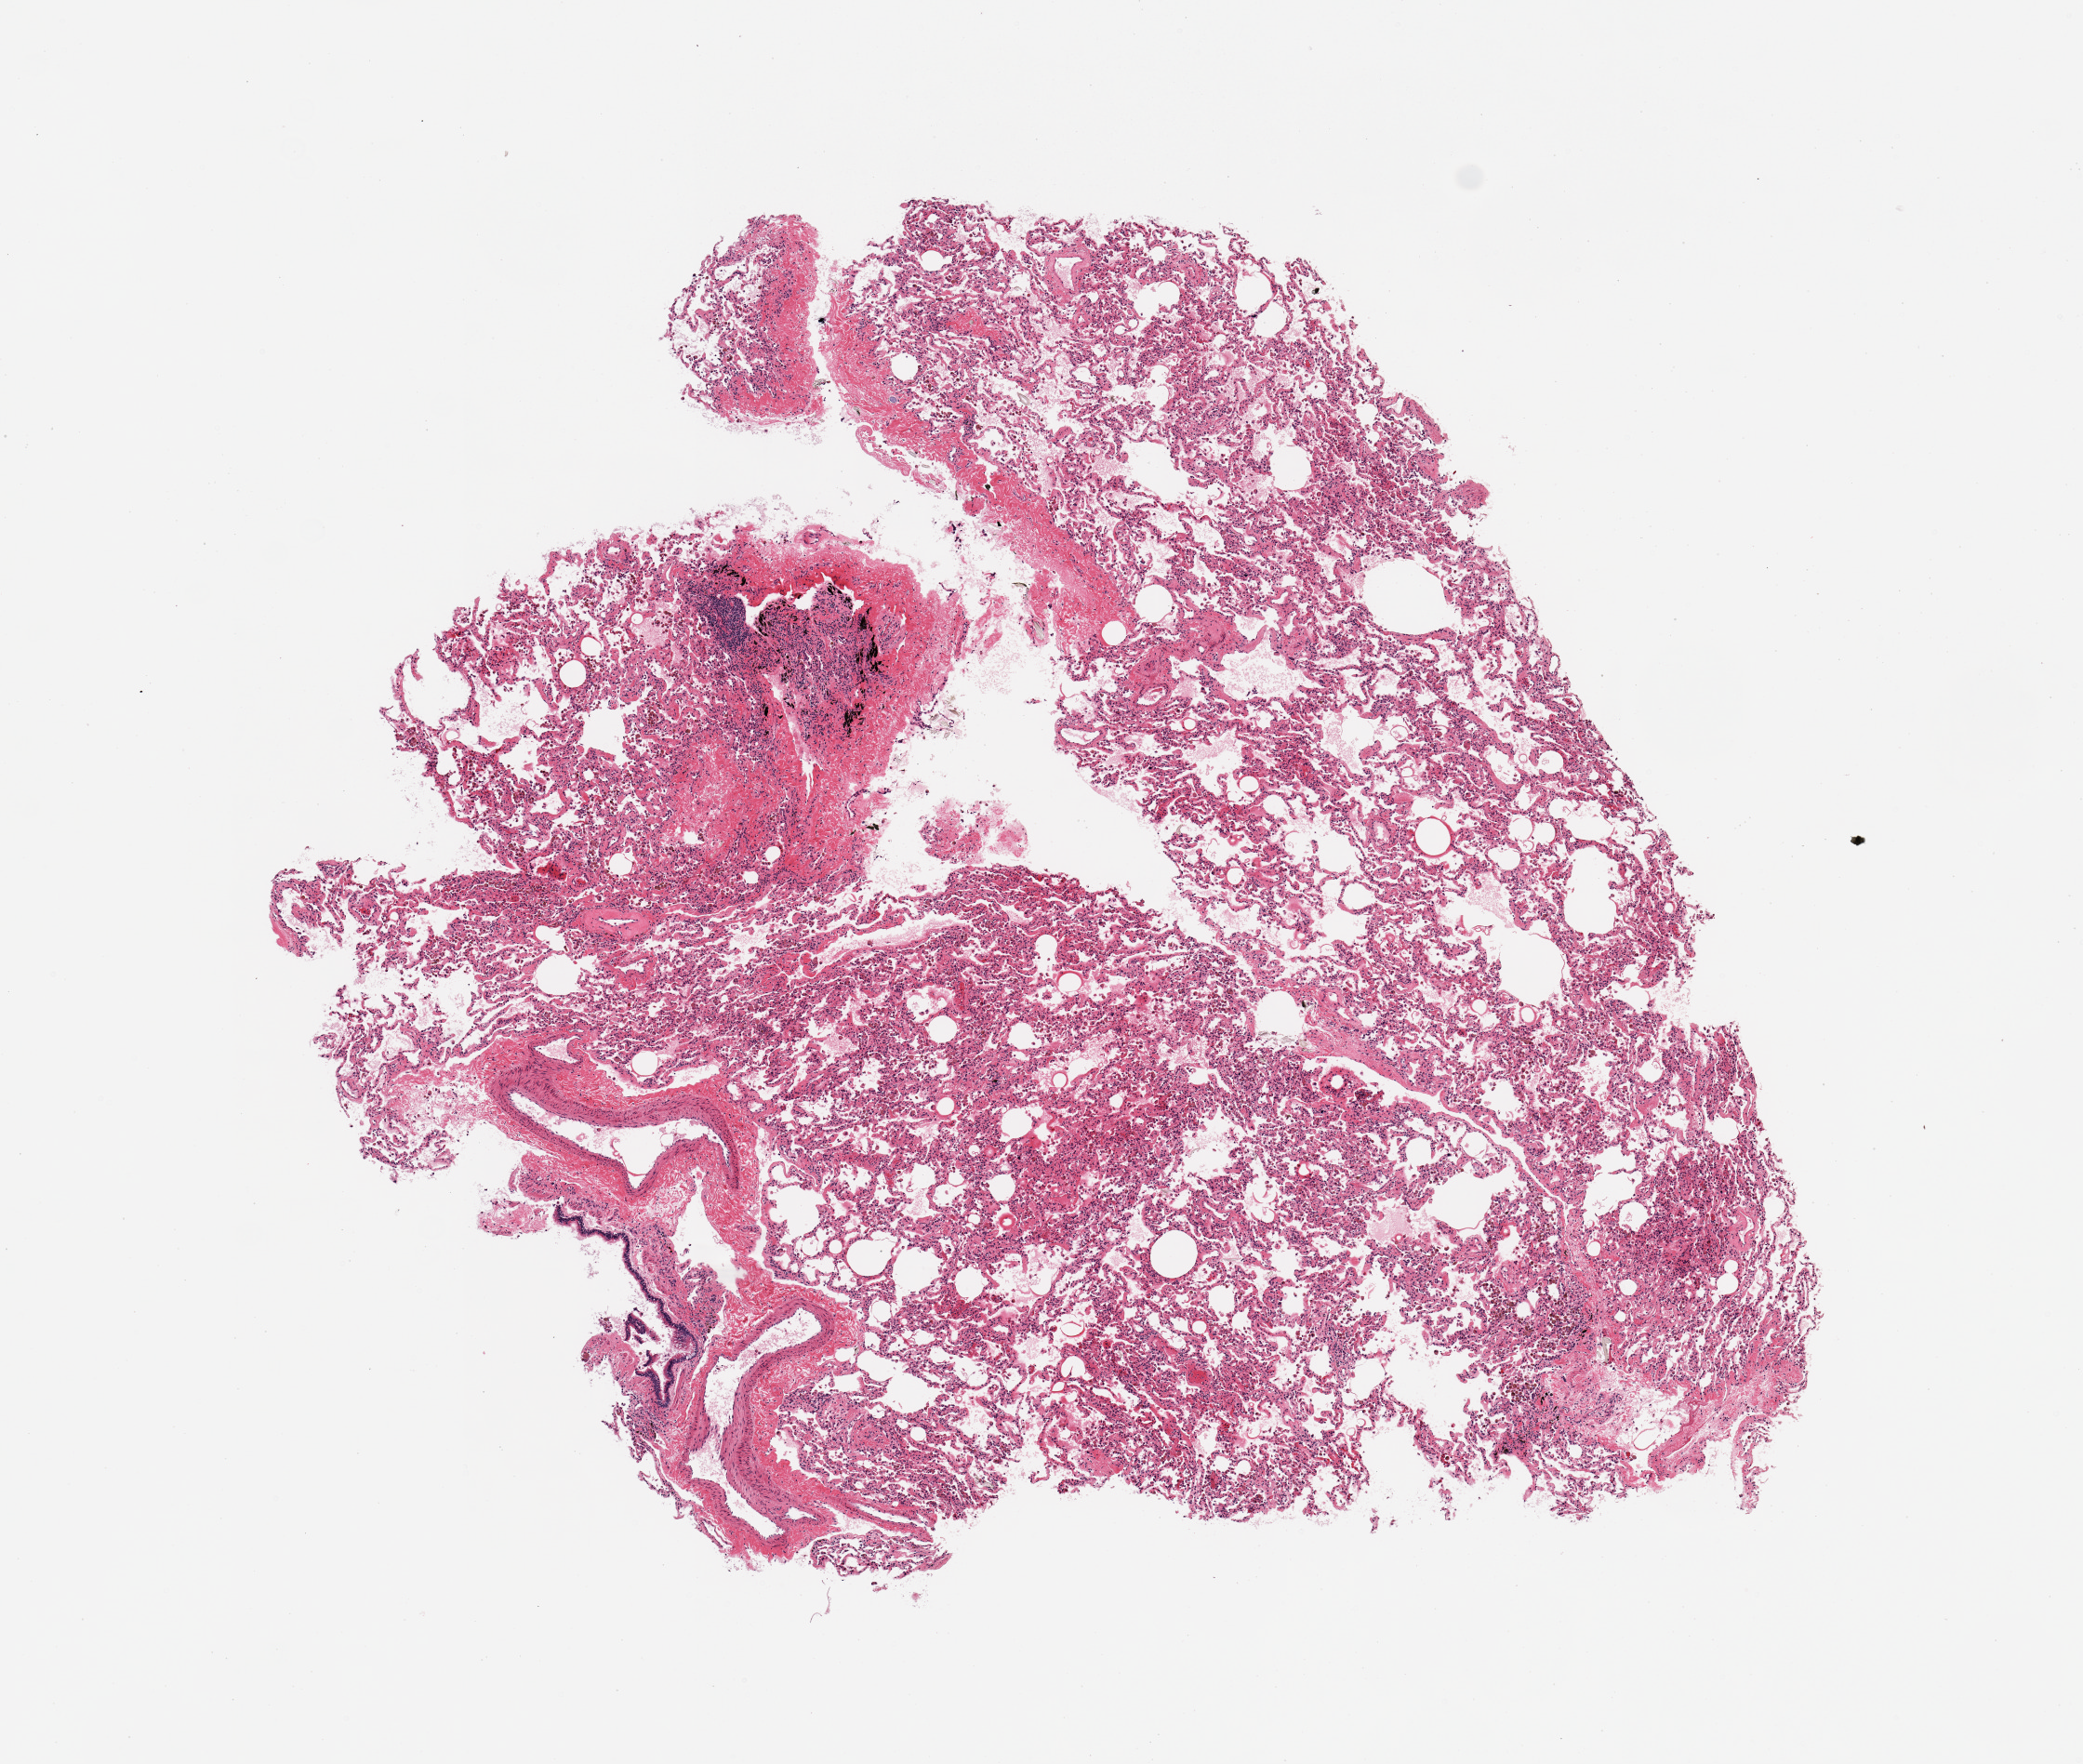
H&E whole-slide image, brightfield — whole scanned area (about 8.9 x 7.5 mm, slide scanned at 20x) shown as a low-resolution overview; PAXgene-fixed, paraffin-embedded tissue; section of lung (target tissue); tissue donor sample.
Pathologist's review note for this sample: 1 pieces; many pigmented macrophages.